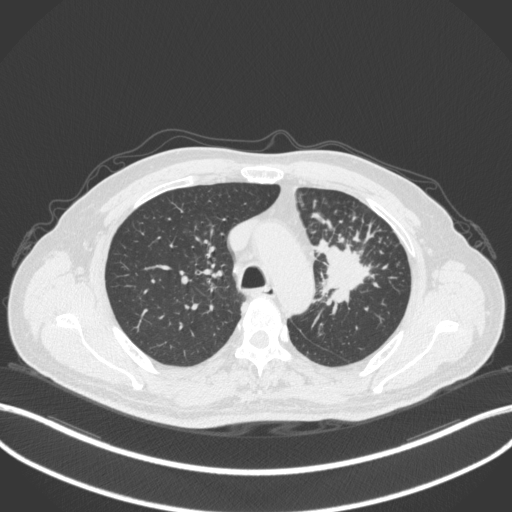
Chest CT, one axial slice. Slice 259 of 386 in the series (ordered by position). Lung window (W 1500 / L -600 HU). 512 × 512 image matrix, field of view 400 × 400 mm. Male patient, age 69 years. Case-level facts recorded for this patient, not image findings: clinical TNM (as recorded): T2a N2 M0.
Outlined on this slice (bounding box drawn by a radiologist):
- lung tumour (recorded histology: adenocarcinoma): bounding box <313,233,379,320> (left, top, right, bottom; pixels)